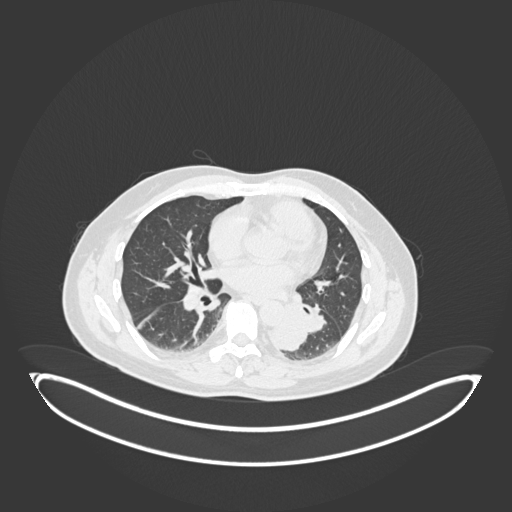
Chest CT, one axial slice. Position 89 of 258 along the scan axis. Reconstruction kernel B30f. 120 kVp. Lung window (W 1500 / L -600 HU). 1 mm slice thickness. 512 × 512 image matrix. Male patient, age 54 years. Case-level facts recorded for this patient, not image findings: clinical TNM (as recorded): T3 N0 M0.
Annotated regions visible in this slice (rectangle marked by the reading radiologist):
- lung tumour (recorded histology: squamous cell carcinoma): bounding box [x1, y1, x2, y2] px = [270, 300, 307, 353]